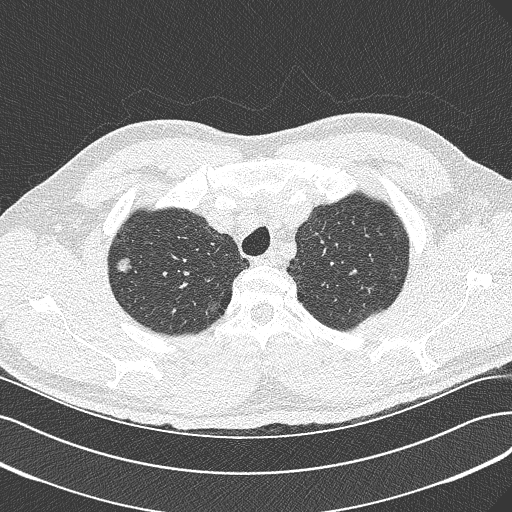
Axial slice from a low-dose chest CT screening exam. First (baseline) screen. Lung window (W 1500 / L -600 HU). 1 mm slice thickness. Lung (sharp) reconstruction kernel (B50f). Slice 48 of 342 in the series. 512 × 512 image matrix. Male, age 56 years at enrolment. Current smoker at enrolment.
- Lesion marked by an expert reader, bounding box [x1, y1, x2, y2] px = [103, 248, 141, 283].
- Screening reader's record for this exam (one nodule recorded; not confirmed to be the boxed lesion): non-calcified nodule or mass ≥4 mm, right upper lobe, 10 × 7 mm, spiculated (stellate) margins, soft tissue attenuation.
- Participant outcome: lung cancer diagnosed 517 days after this screen — bronchiolo-alveolar carcinoma, non-mucinous, right upper lobe, moderately differentiated (G2), stage IIIB (AJCC 6th edition), 10 mm at pathology.